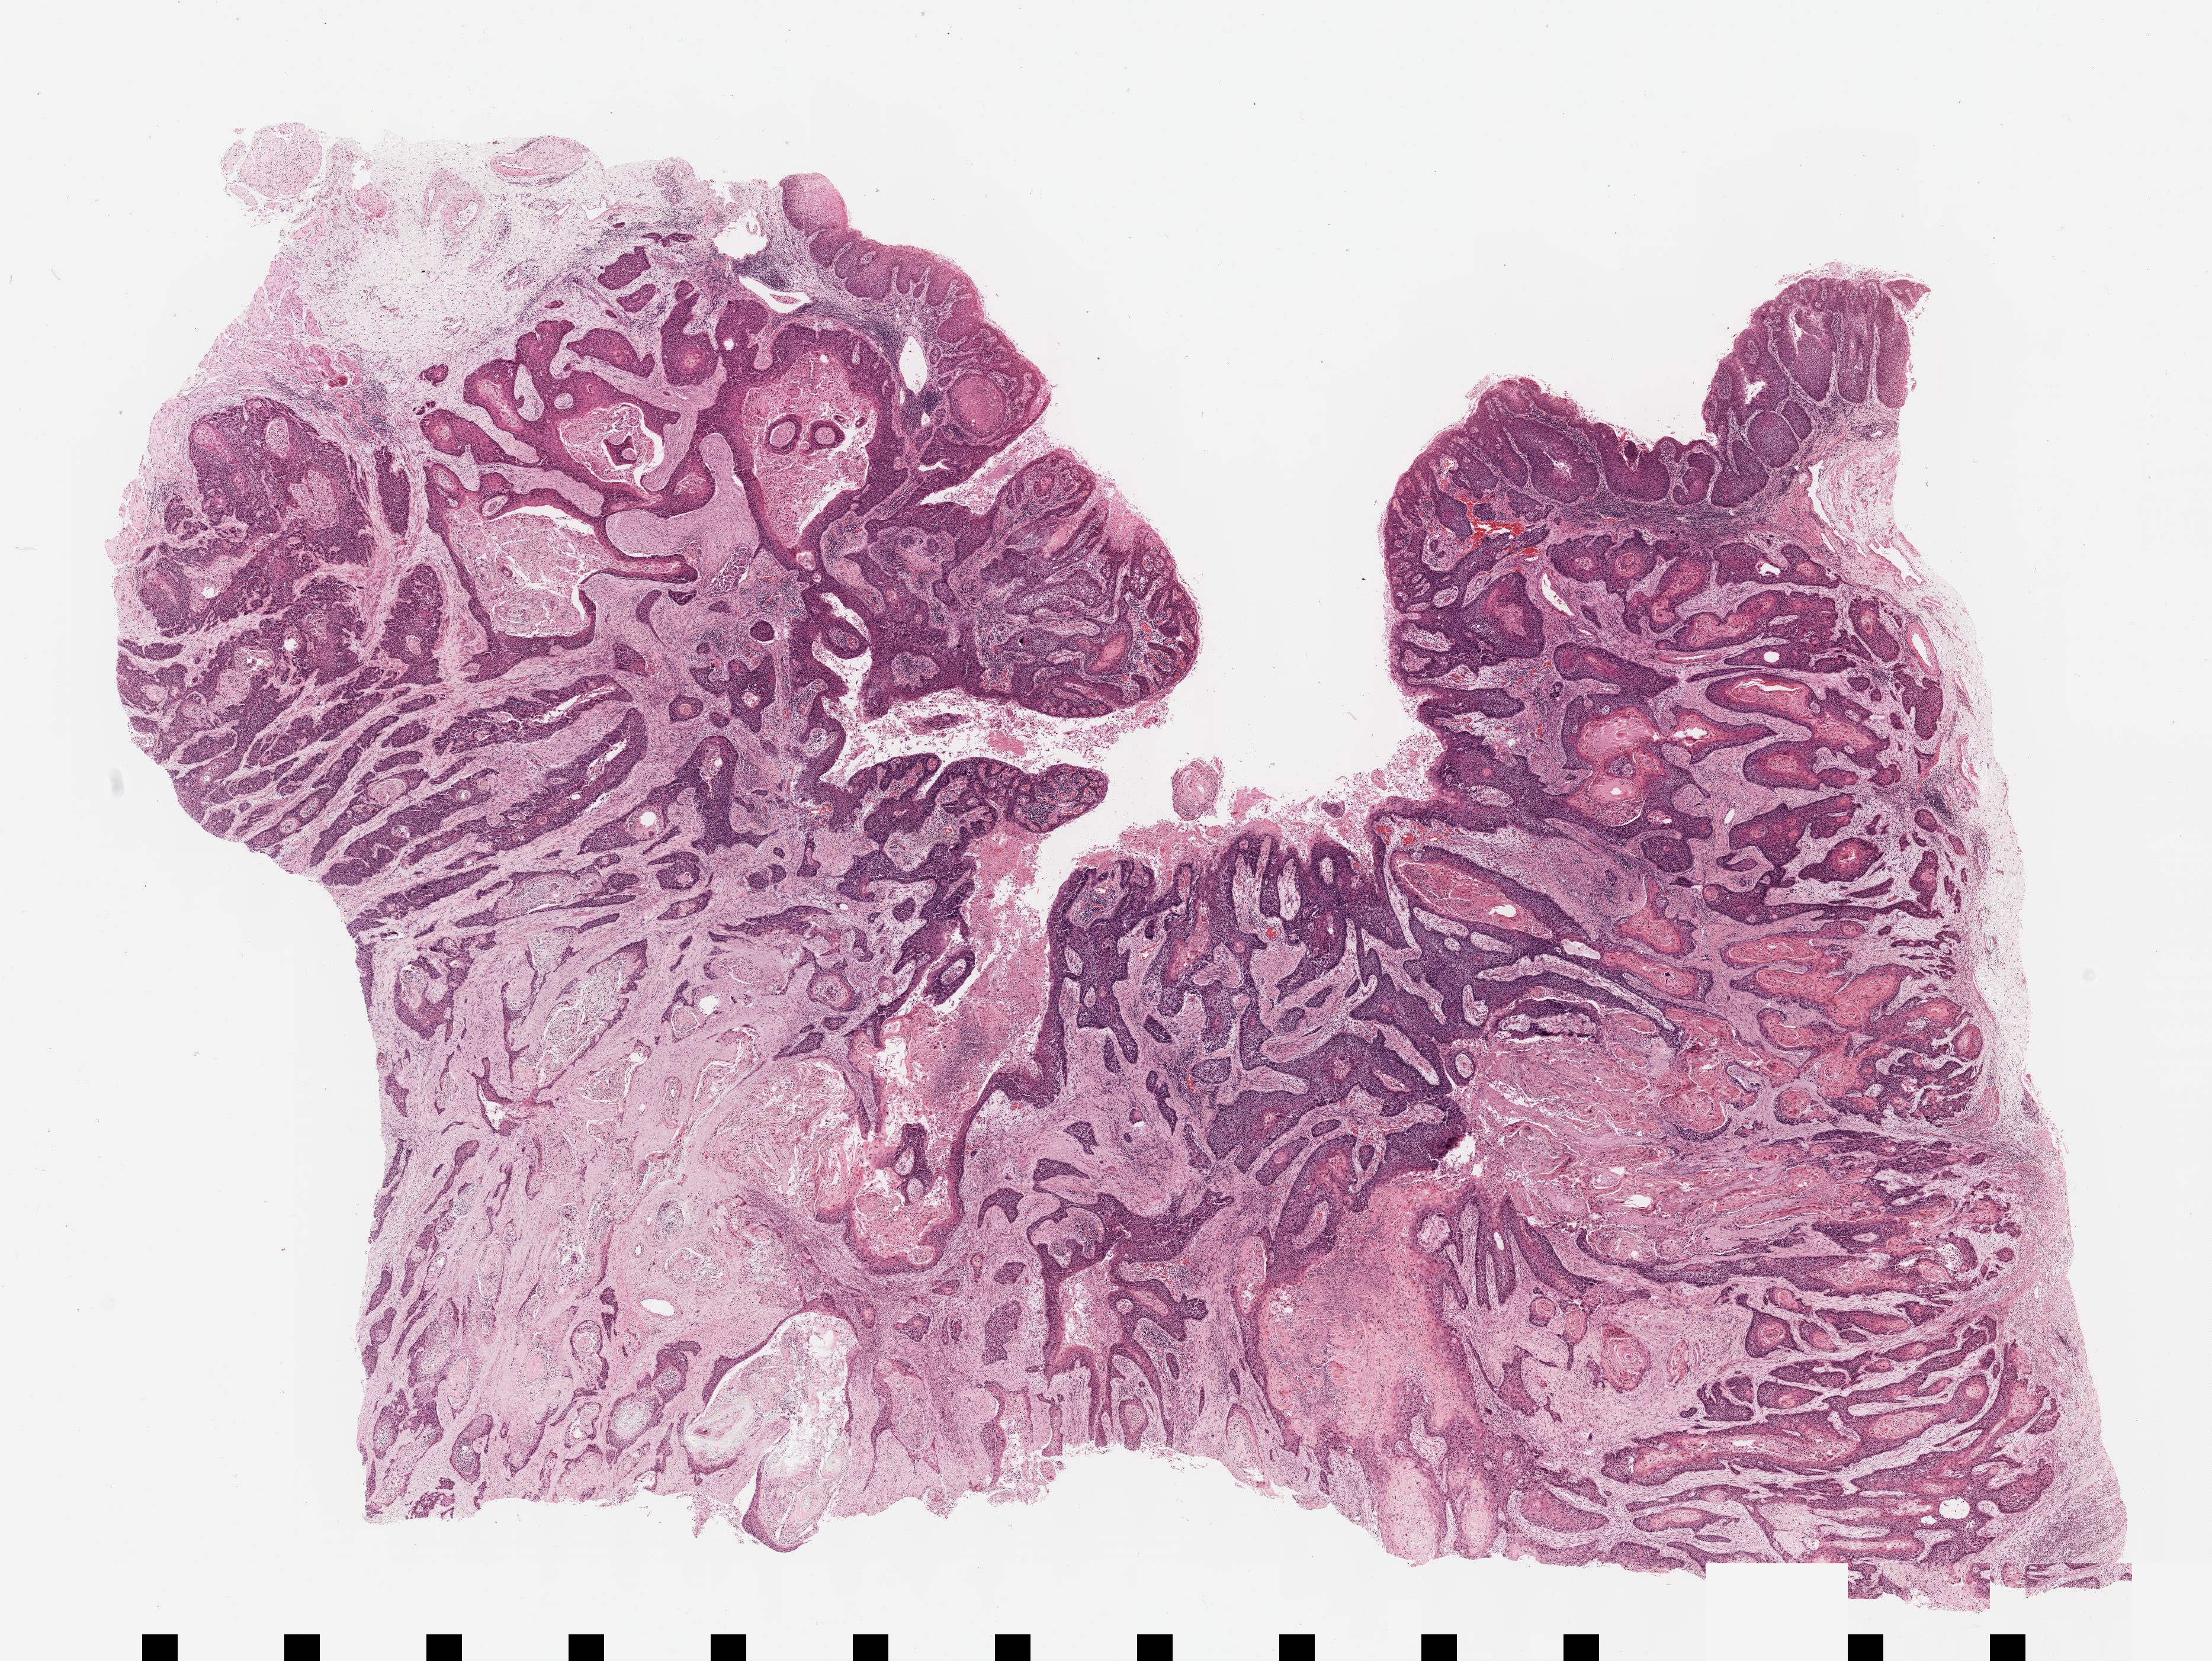
Whole-slide histology image, Hematoxylin and eosin (H&E) stained — shown as a low-resolution overview of the whole scanned area (about 15.1 x 11.3 mm, slide scanned at 40x); formalin-fixed paraffin-embedded (FFPE) diagnostic section; esophagus, primary tumour sample. Male patient; age at initial diagnosis 53 years. Histologic grade: G2 (moderately differentiated).
- histologic diagnosis: Squamous cell carcinoma, NOS
- AJCC pathologic stage: IIIA (7th edition)